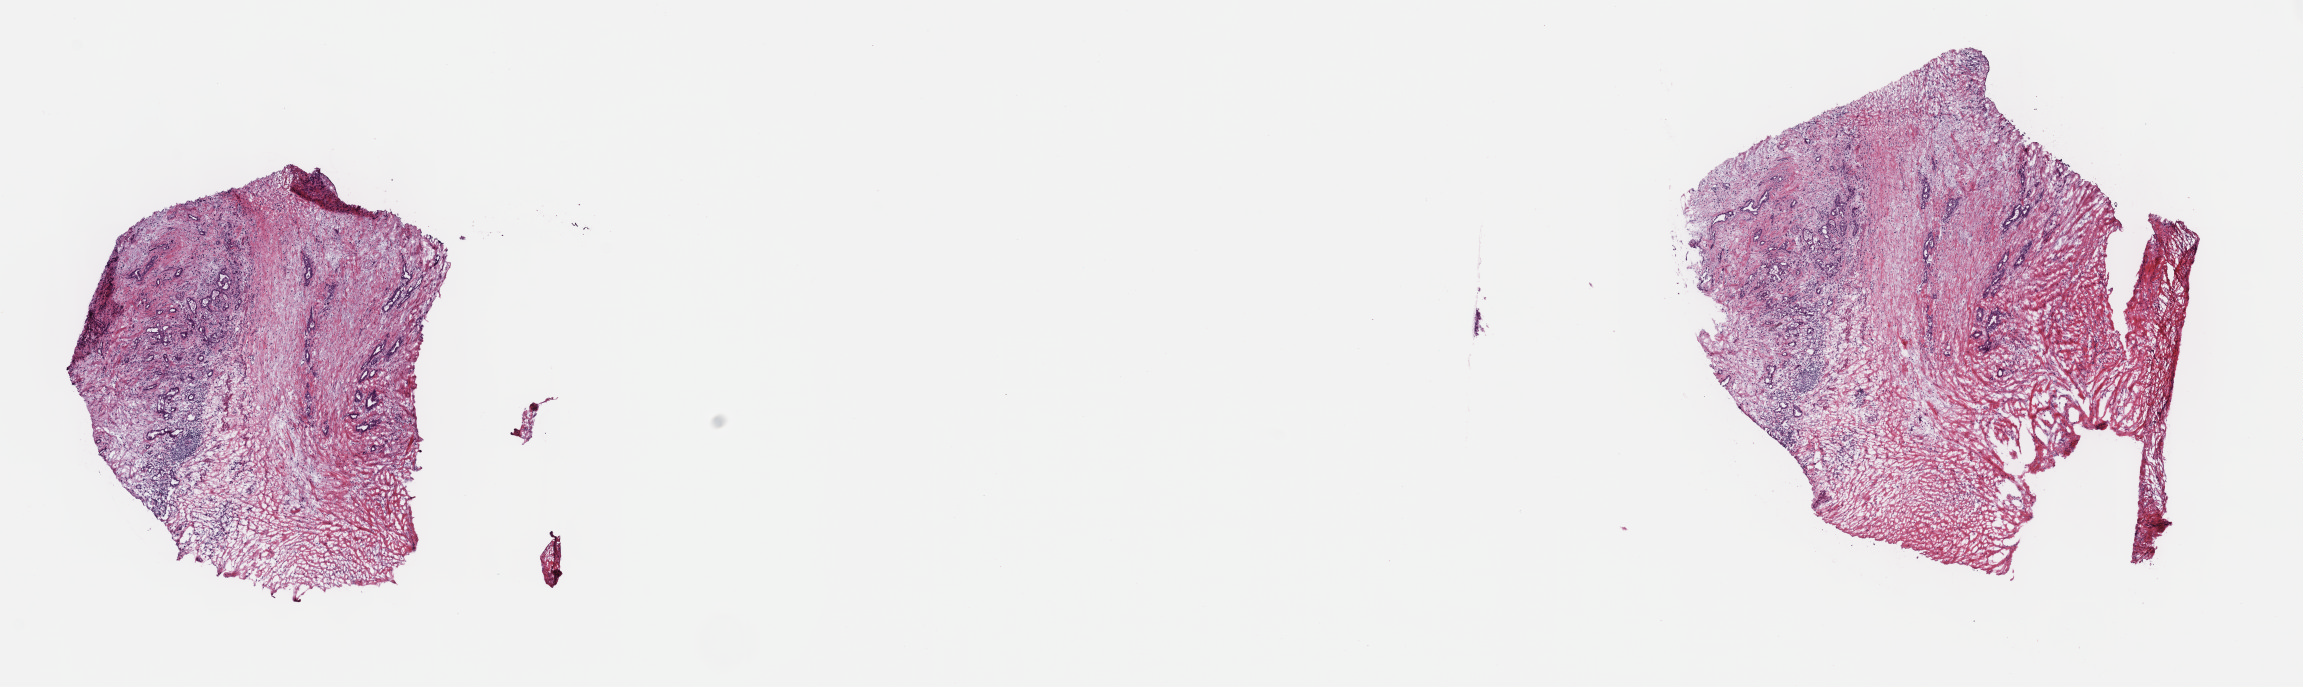
Digitized H&E-stained tissue section (whole slide), whole scanned area (about 18.6 x 5.6 mm, from a 40x scan) shown as a low-resolution overview; frozen section from the top of the tissue portion; pancreas, primary tumour sample. Female patient; age at initial diagnosis 49 years. Histologic grade: G2 (moderately differentiated). Slide review estimates, as recorded: tumour cells 40%, tumour nuclei 40%, normal cells 10%, stromal cells 50%, necrosis 0%. Inflammatory infiltration, as recorded: lymphocyte infiltration 40%, monocyte infiltration 20%, neutrophil infiltration 20%.
- lymph nodes positive (case pathology): 0 of 21 examined
- AJCC pathologic stage: III (7th edition)
- histologic diagnosis: Infiltrating duct carcinoma, NOS (head of pancreas)